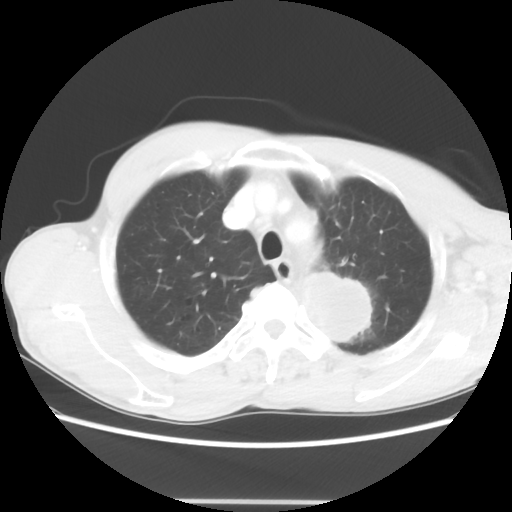
Chest CT, one axial slice; position 52 of 62 along the scan axis; reconstruction kernel STANDARD; lung window (W 1500 / L -600 HU); 512 × 512 image matrix, field of view 360 × 360 mm. Male patient, age 61 years. Case-level facts recorded for this patient, not image findings: clinical TNM (as recorded): T3 N1 M1.
Outlined on this slice (rectangle marked by the reading radiologist):
- lung tumour (recorded histology: adenocarcinoma): bounding box [x1, y1, x2, y2] px = [299, 262, 375, 350]